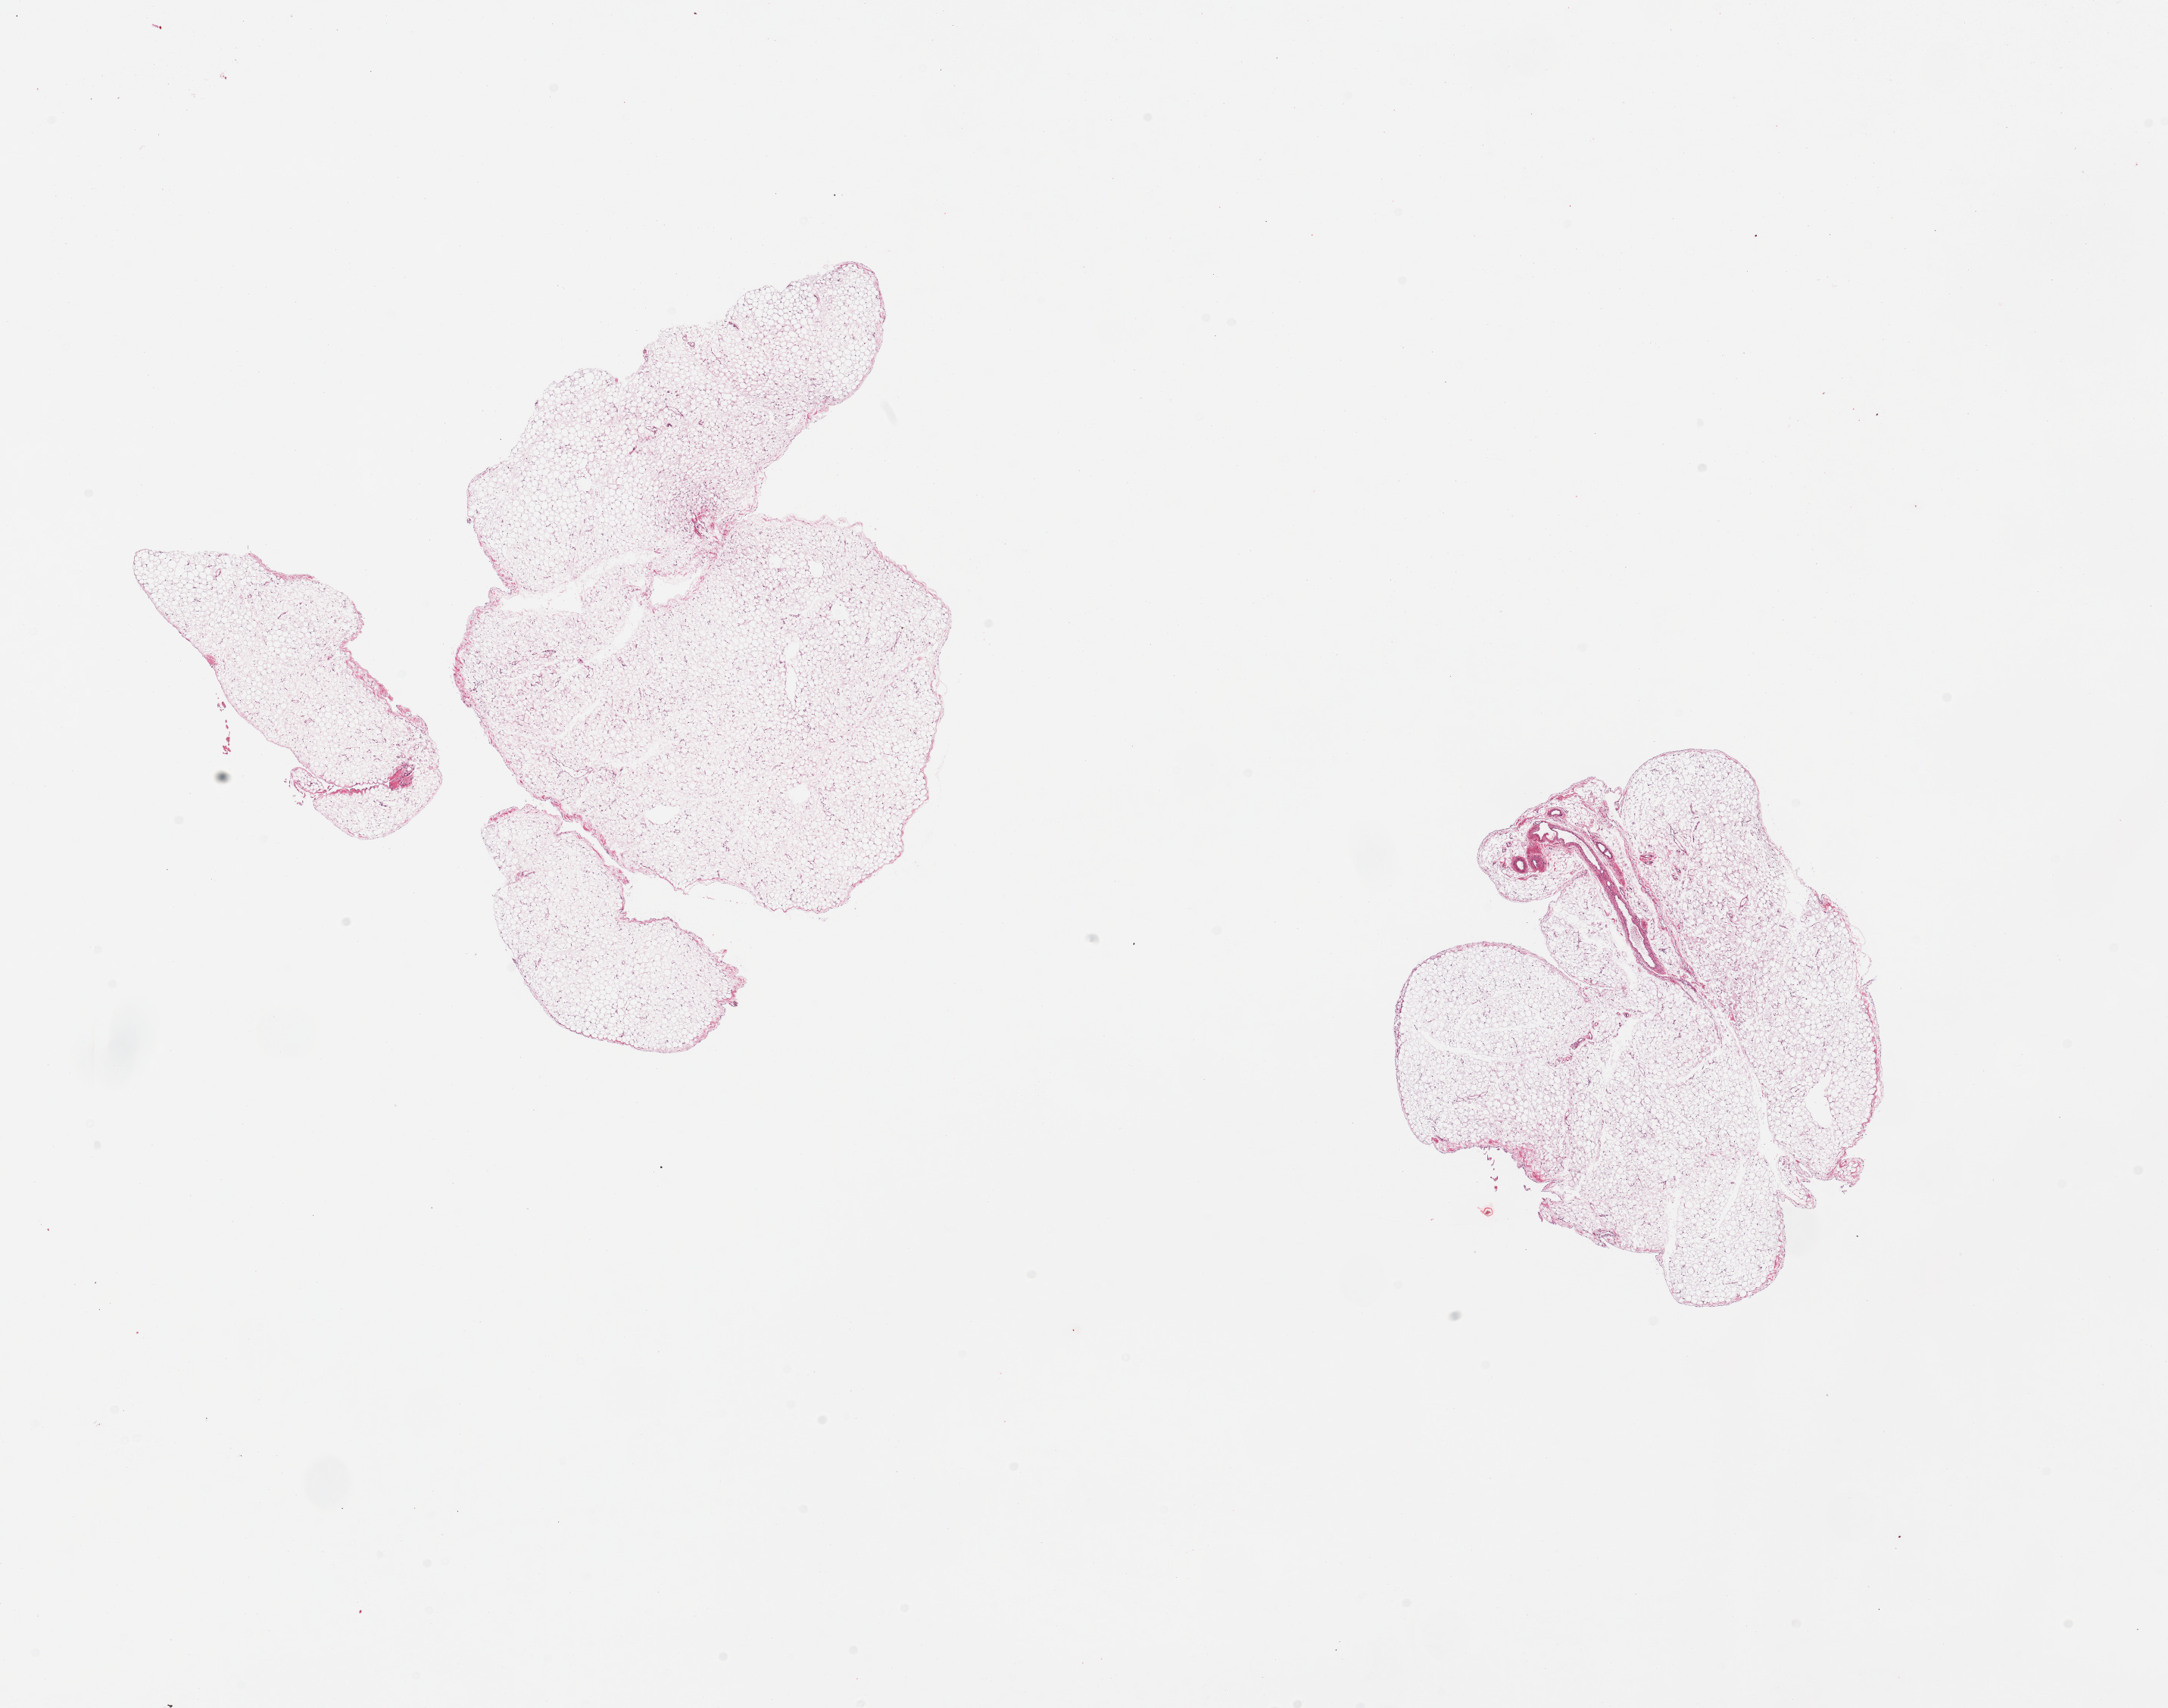
Digitized haematoxylin and eosin-stained section — low-resolution overview of the scanned area, about 22.6 x 17.8 mm, PAXgene-fixed, paraffin-embedded tissue, sampled site (target tissue): omentum, donor tissue sample.
• pathologist's review note for this sample: 2 pieces